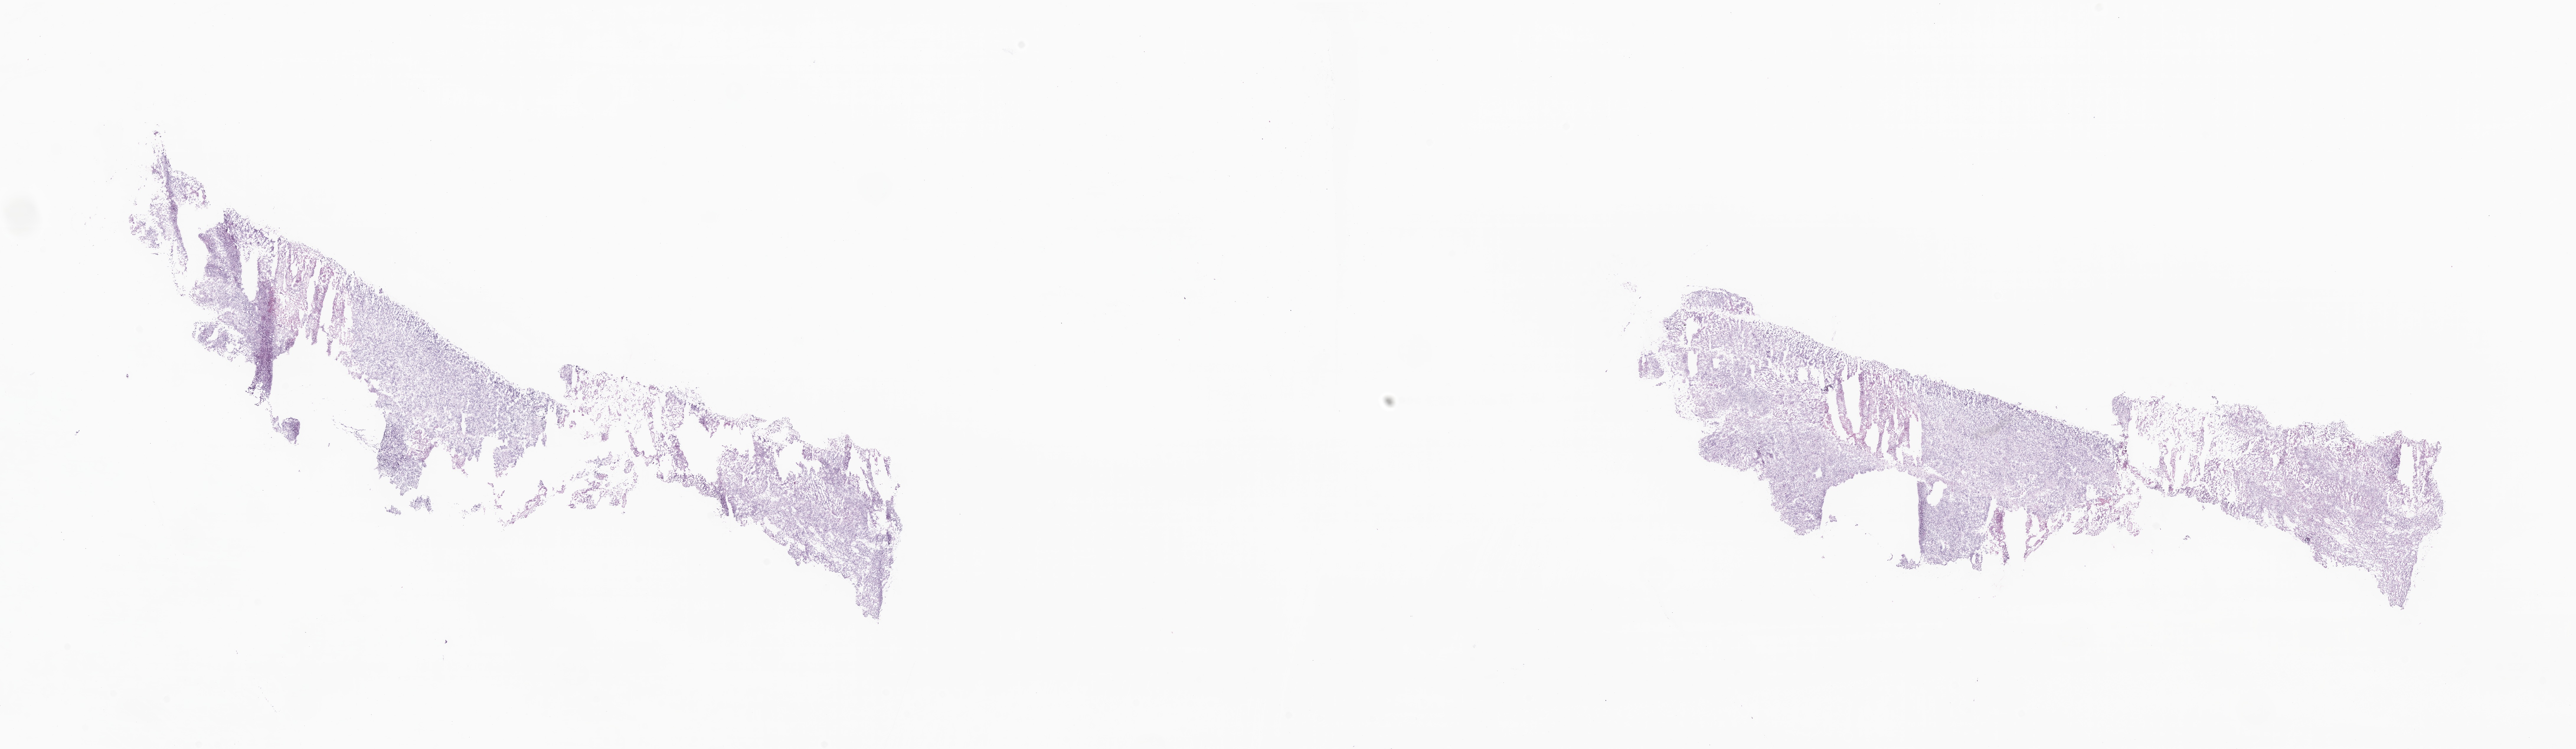
Digitized H&E-stained section of tumor tissue from the brain — whole scanned area (about 36.8 x 10.7 mm) shown as a low-resolution overview. Frozen section (OCT-embedded). Male patient, age 168 months (14 years).
Recorded diagnosis: Glioma, malignant.